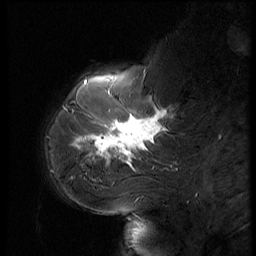
Breast MRI (dynamic contrast-enhanced), one sagittal slice. Slice 16 of 56 in the series (ordered by position). Dynamic contrast-enhanced series, image 2 of 3 at this slice position (ordered by acquisition). 1.5 T. TE 4.2 ms, TR 9 ms. 256 × 256 image matrix, field of view 180 × 180 mm. Female patient, age 61 years. From the clinical record (not read from this slice): setting: breast cancer imaged before/during neoadjuvant chemotherapy; receptor status: HR-positive, HER2-negative.
Structures marked on this image (semi-automatic segmentation, software-assisted and operator-edited):
- analysis volume of interest (the breast-tissue region the enhancement analysis was run in; not a lesion): bounding box (x1, y1, x2, y2) in pixels: (65, 74, 185, 175)
- tumour enhancement mask (voxels above the 140 % enhancement threshold inside the analysis volume of interest): (79, 92, 168, 168)